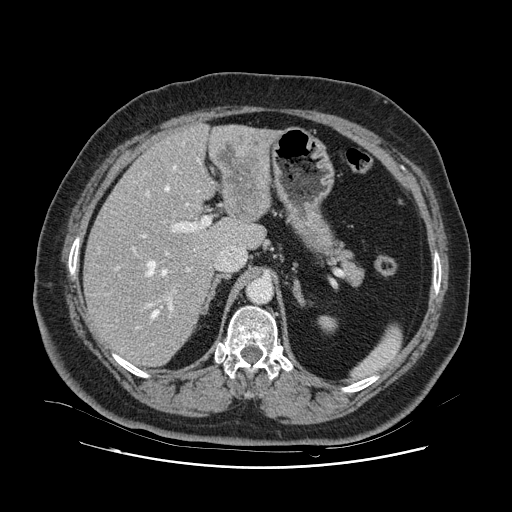
Contrast-enhanced abdominal CT, one axial slice. Position 71 of 132 along the scan axis. 120 kVp. Intravenous contrast given. Soft-tissue window (W 400 / L 40 HU). 2.5 mm slice thickness. 512 × 512 image matrix. Female patient, age 73 years. From the clinical record (not read from this slice): diagnosis: colorectal cancer liver metastases, imaged before liver resection; multiple liver metastases: no.
Annotated regions visible in this slice (expert manual segmentation):
- hepatic veins: bounding box (x1, y1, x2, y2) in pixels: (98, 143, 199, 329)
- liver: (85, 125, 272, 367)
- planned liver remnant (the part of the liver to remain after resection): (85, 155, 243, 366)
- portal vein (with intrahepatic branches): (116, 192, 211, 311)
- liver metastasis: (217, 143, 260, 212)